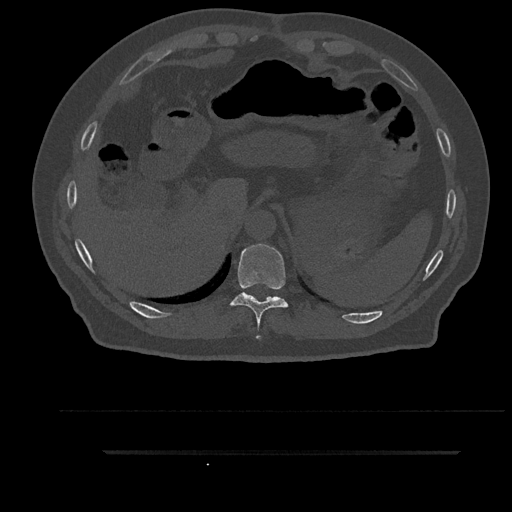
CT including the spine, one axial slice. Position 359 of 797 along the scan axis. Bone window (W 1800 / L 400 HU). 0.5 mm slice thickness. 512 × 512 image matrix, field of view 432 × 432 mm. Male patient, age 63 years. From the clinical record (not read from this slice): primary cancer: renal; vertebrae with lytic lesions (as recorded): T8.
Annotated regions visible in this slice (semi-automatically segmented with operator editing):
- T10 vertebra: box from (x=230, y=244) to (x=288, y=339) px